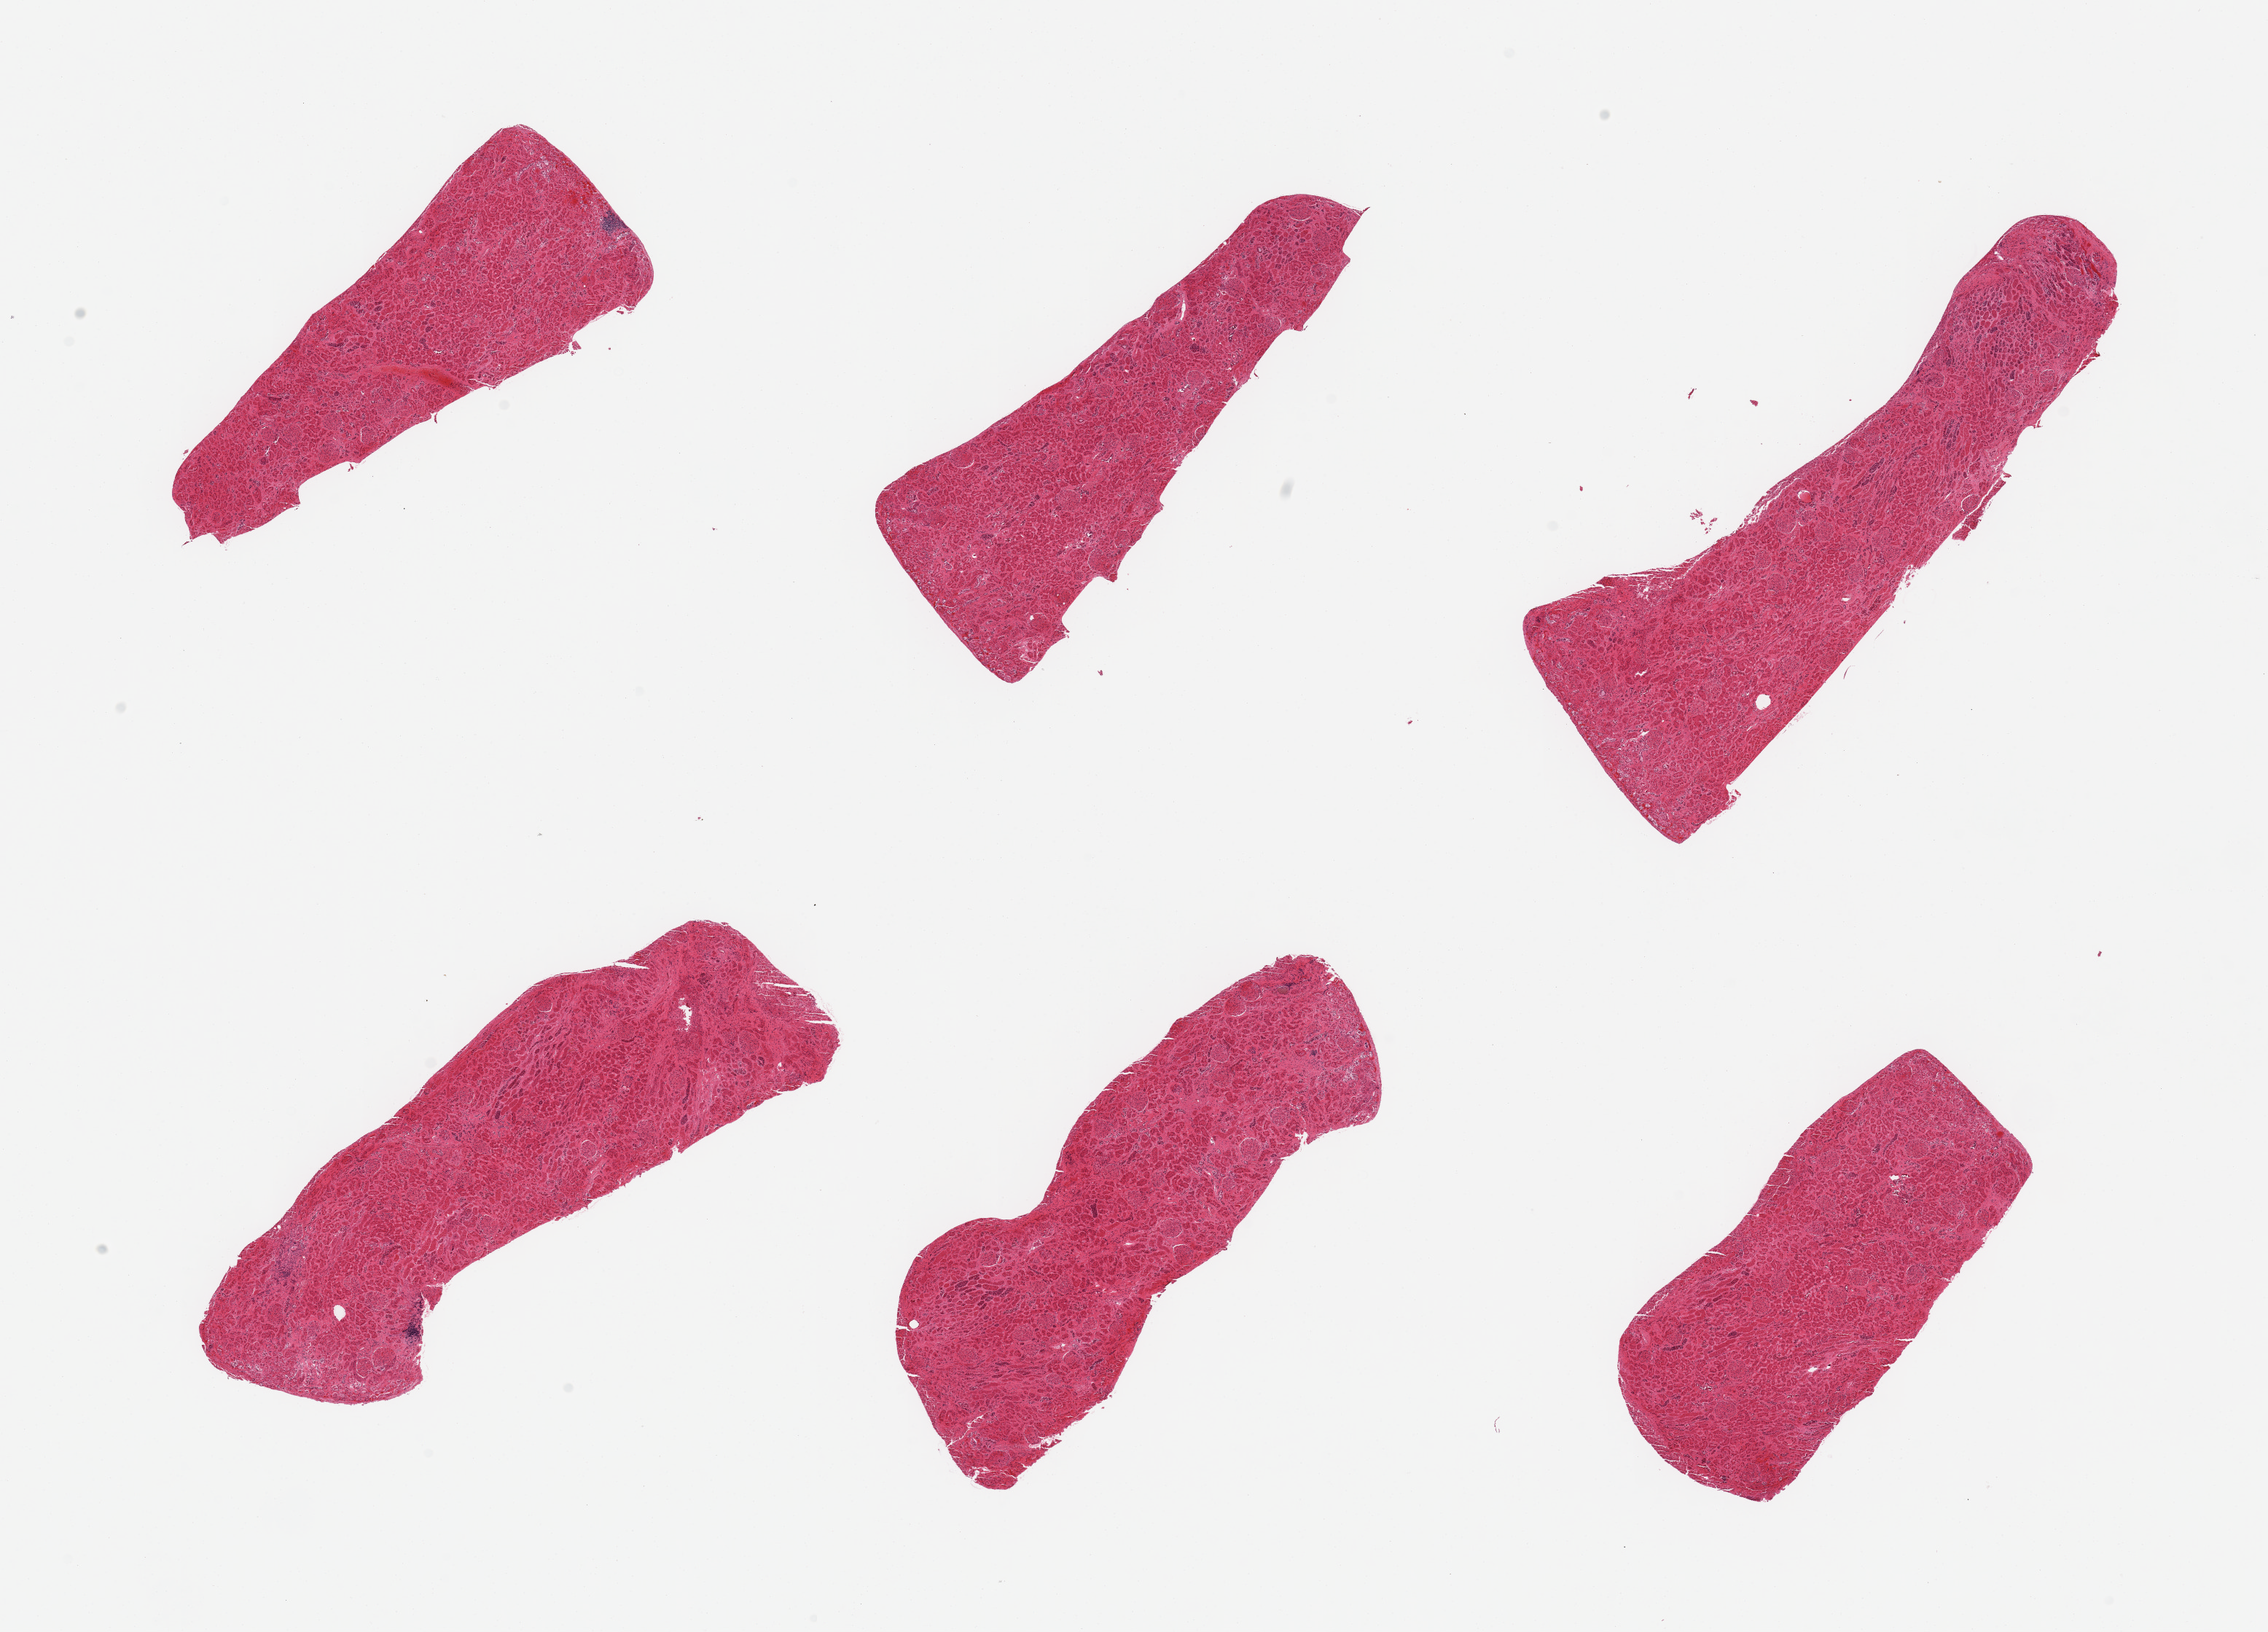
Whole-slide image, haematoxylin and eosin stain, brightfield — shown as a low-resolution overview of the whole scanned area (about 24.6 x 17.7 mm, acquisition: 20x scan), PAXgene-fixed, paraffin-embedded tissue, sampled site (target tissue): renal cortex, donor tissue sample. Donor: male.
Review note (as recorded): 6 pieces; marked congestion.